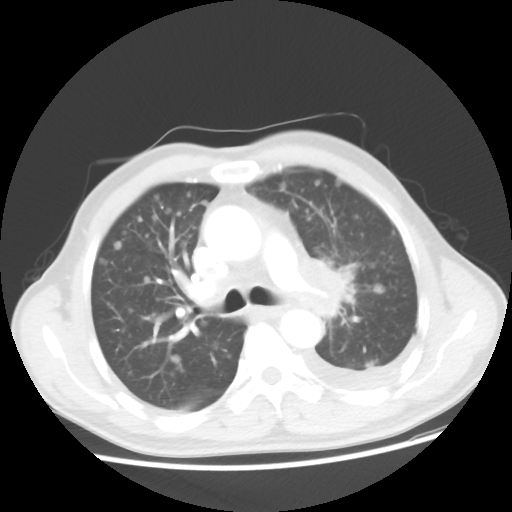
Chest CT, one axial slice; reconstruction kernel STANDARD; 100 kVp; lung window (W 1500 / L -600 HU); 512 × 512 image matrix, field of view 362 × 362 mm. Patient: male, 55 years. Case-level facts recorded for this patient, not image findings: clinical TNM (as recorded): T2 N3 M1a.
Outlined on this slice (rectangle marked by the reading radiologist):
- lung tumour (recorded histology: squamous cell carcinoma): box from (x=312, y=252) to (x=355, y=324) px